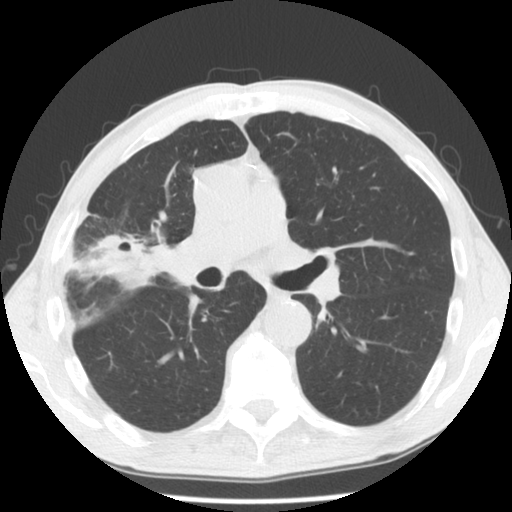
Low-dose screening chest CT, axial slice. Third screening round (two years after baseline). Lung window (W 1500 / L -600 HU). 2.5 mm slice thickness. Standard (soft-tissue) reconstruction kernel (STANDARD). Male participant, aged 57 years at enrolment.
Lesion marked by an expert reader, box from (x=59, y=211) to (x=163, y=309) px. The exam's reader record, not a measurement of the box and not confirmed to be the same lesion: non-calcified nodule or mass ≥4 mm, right upper lobe, 38 × 34 mm, poorly defined margins, mixed attenuation, pre-existing on the prior screen: no. Later outcome: lung cancer diagnosed 76 days after this screen — squamous cell carcinoma, NOS, right upper lobe, stage IA (AJCC 6th edition), 15 mm at pathology.